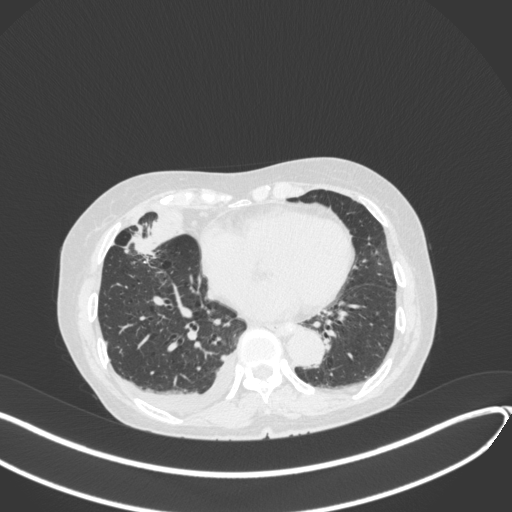
Chest CT, one axial slice; slice 141 of 418 in the series (ordered by position); 120 kVp; lung window (W 1500 / L -600 HU); 1 mm slice thickness; 512 × 512 image matrix, field of view 400 × 400 mm. Patient: female, 75 years. Case-level facts recorded for this patient, not image findings: clinical TNM (as recorded): T2a N3 M0.
Annotated regions visible in this slice (bounding box drawn by a radiologist):
- lung tumour (recorded histology: adenocarcinoma): box from (x=126, y=225) to (x=167, y=258) px